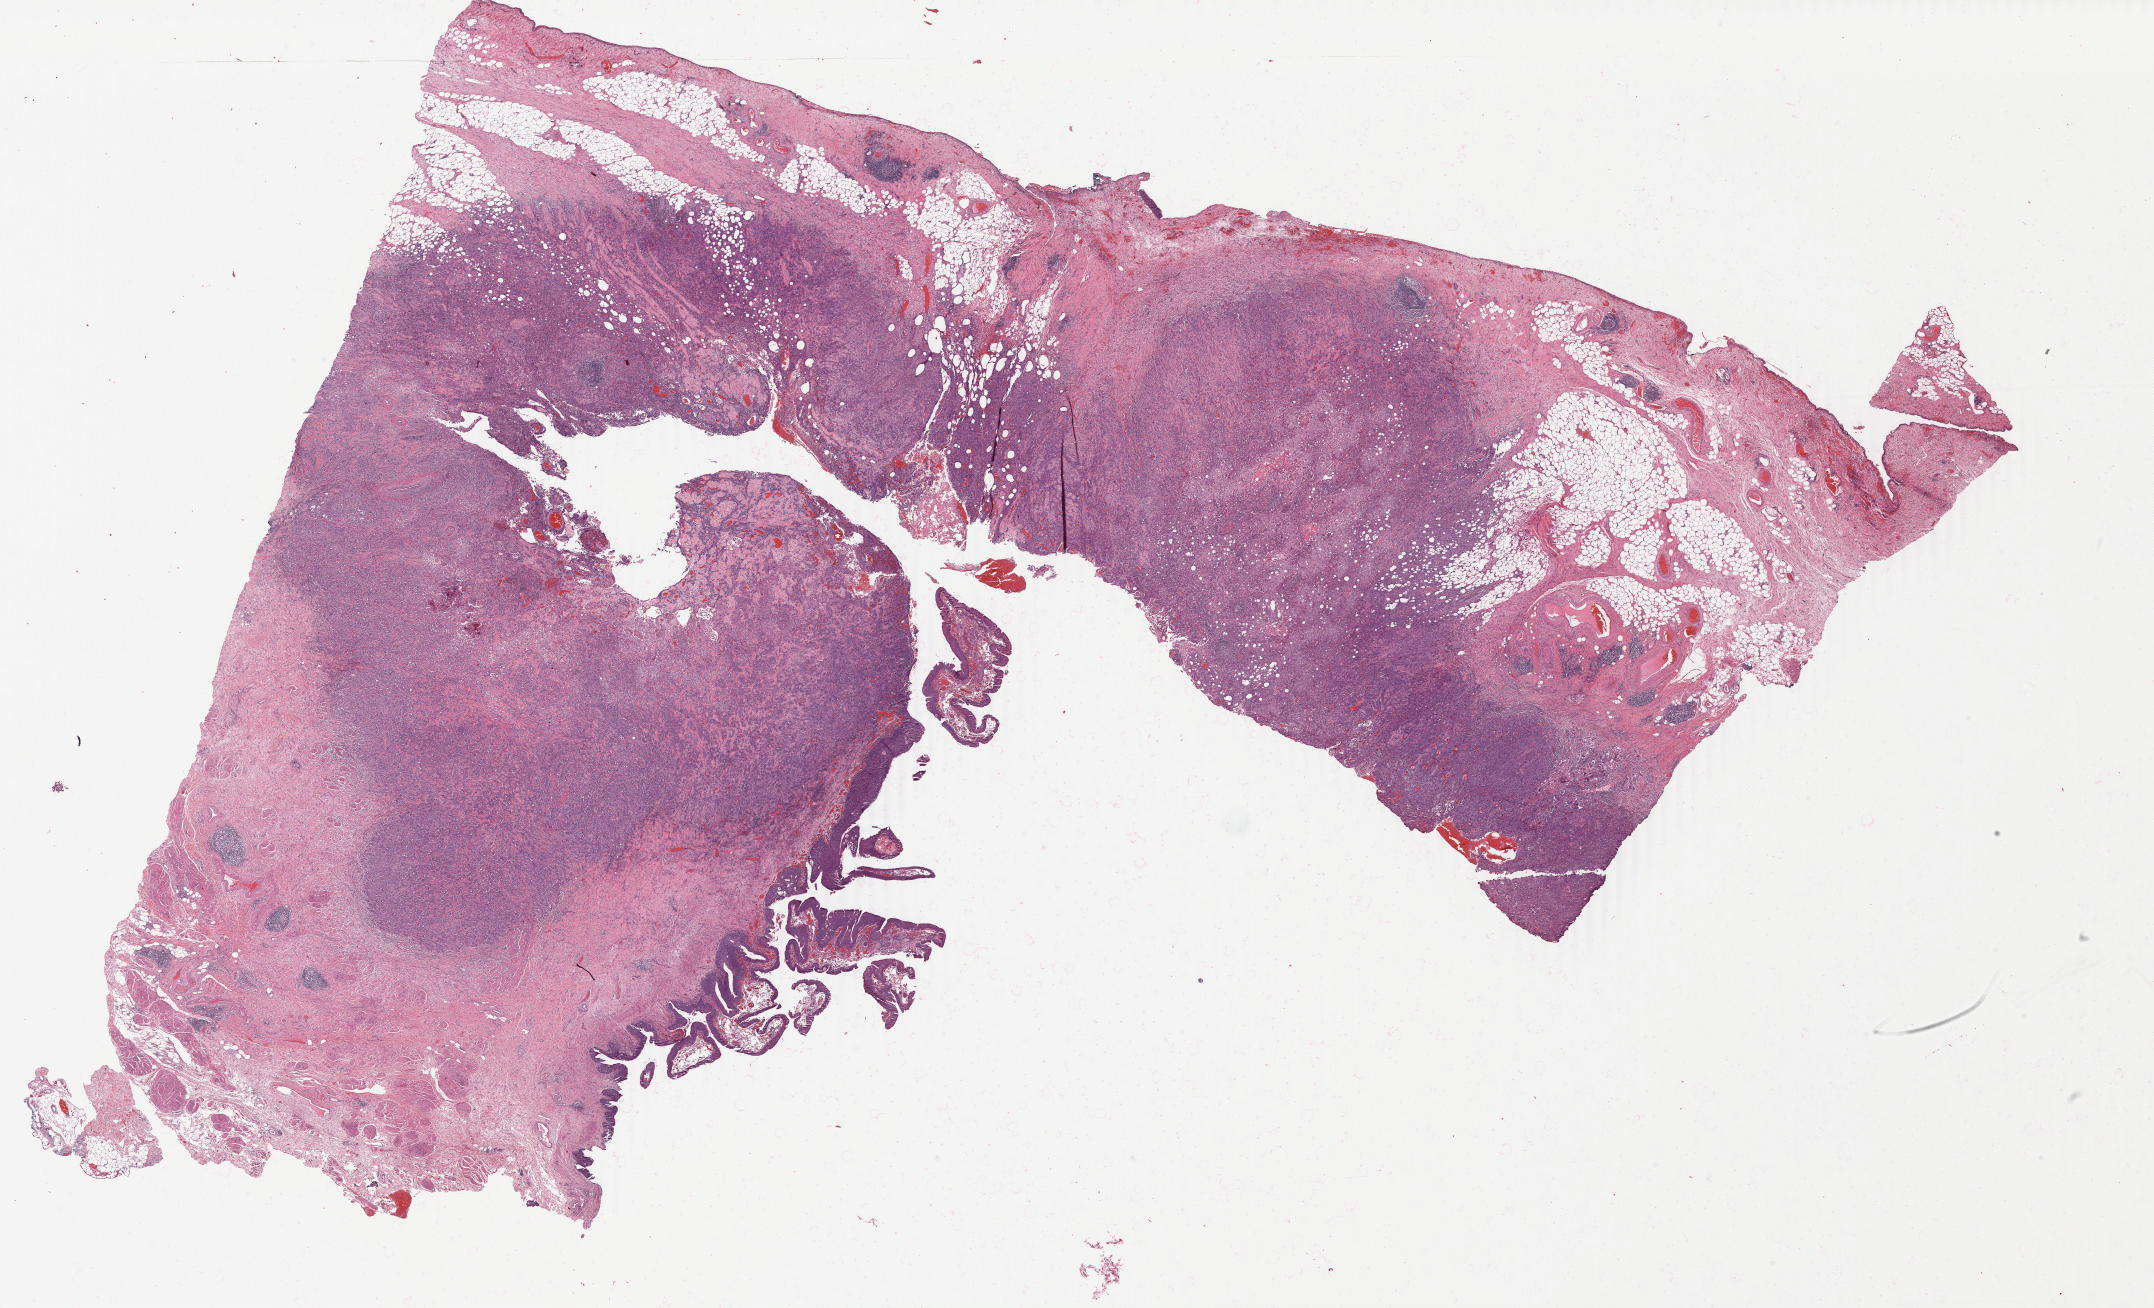
Digitized H&E tissue section (whole slide) — low-resolution overview of the scanned area, about 34.3 x 20.8 mm (slide scanned at 40x); formalin-fixed paraffin-embedded (FFPE) diagnostic section; bladder, primary tumour sample. Female patient; age at initial diagnosis 75 years. Histologic grade: high grade.
- AJCC pathologic stage: III (7th edition)
- lymph nodes positive (case pathology): 0 of 12 examined
- pathologic diagnosis: Transitional cell carcinoma (posterior wall of bladder)